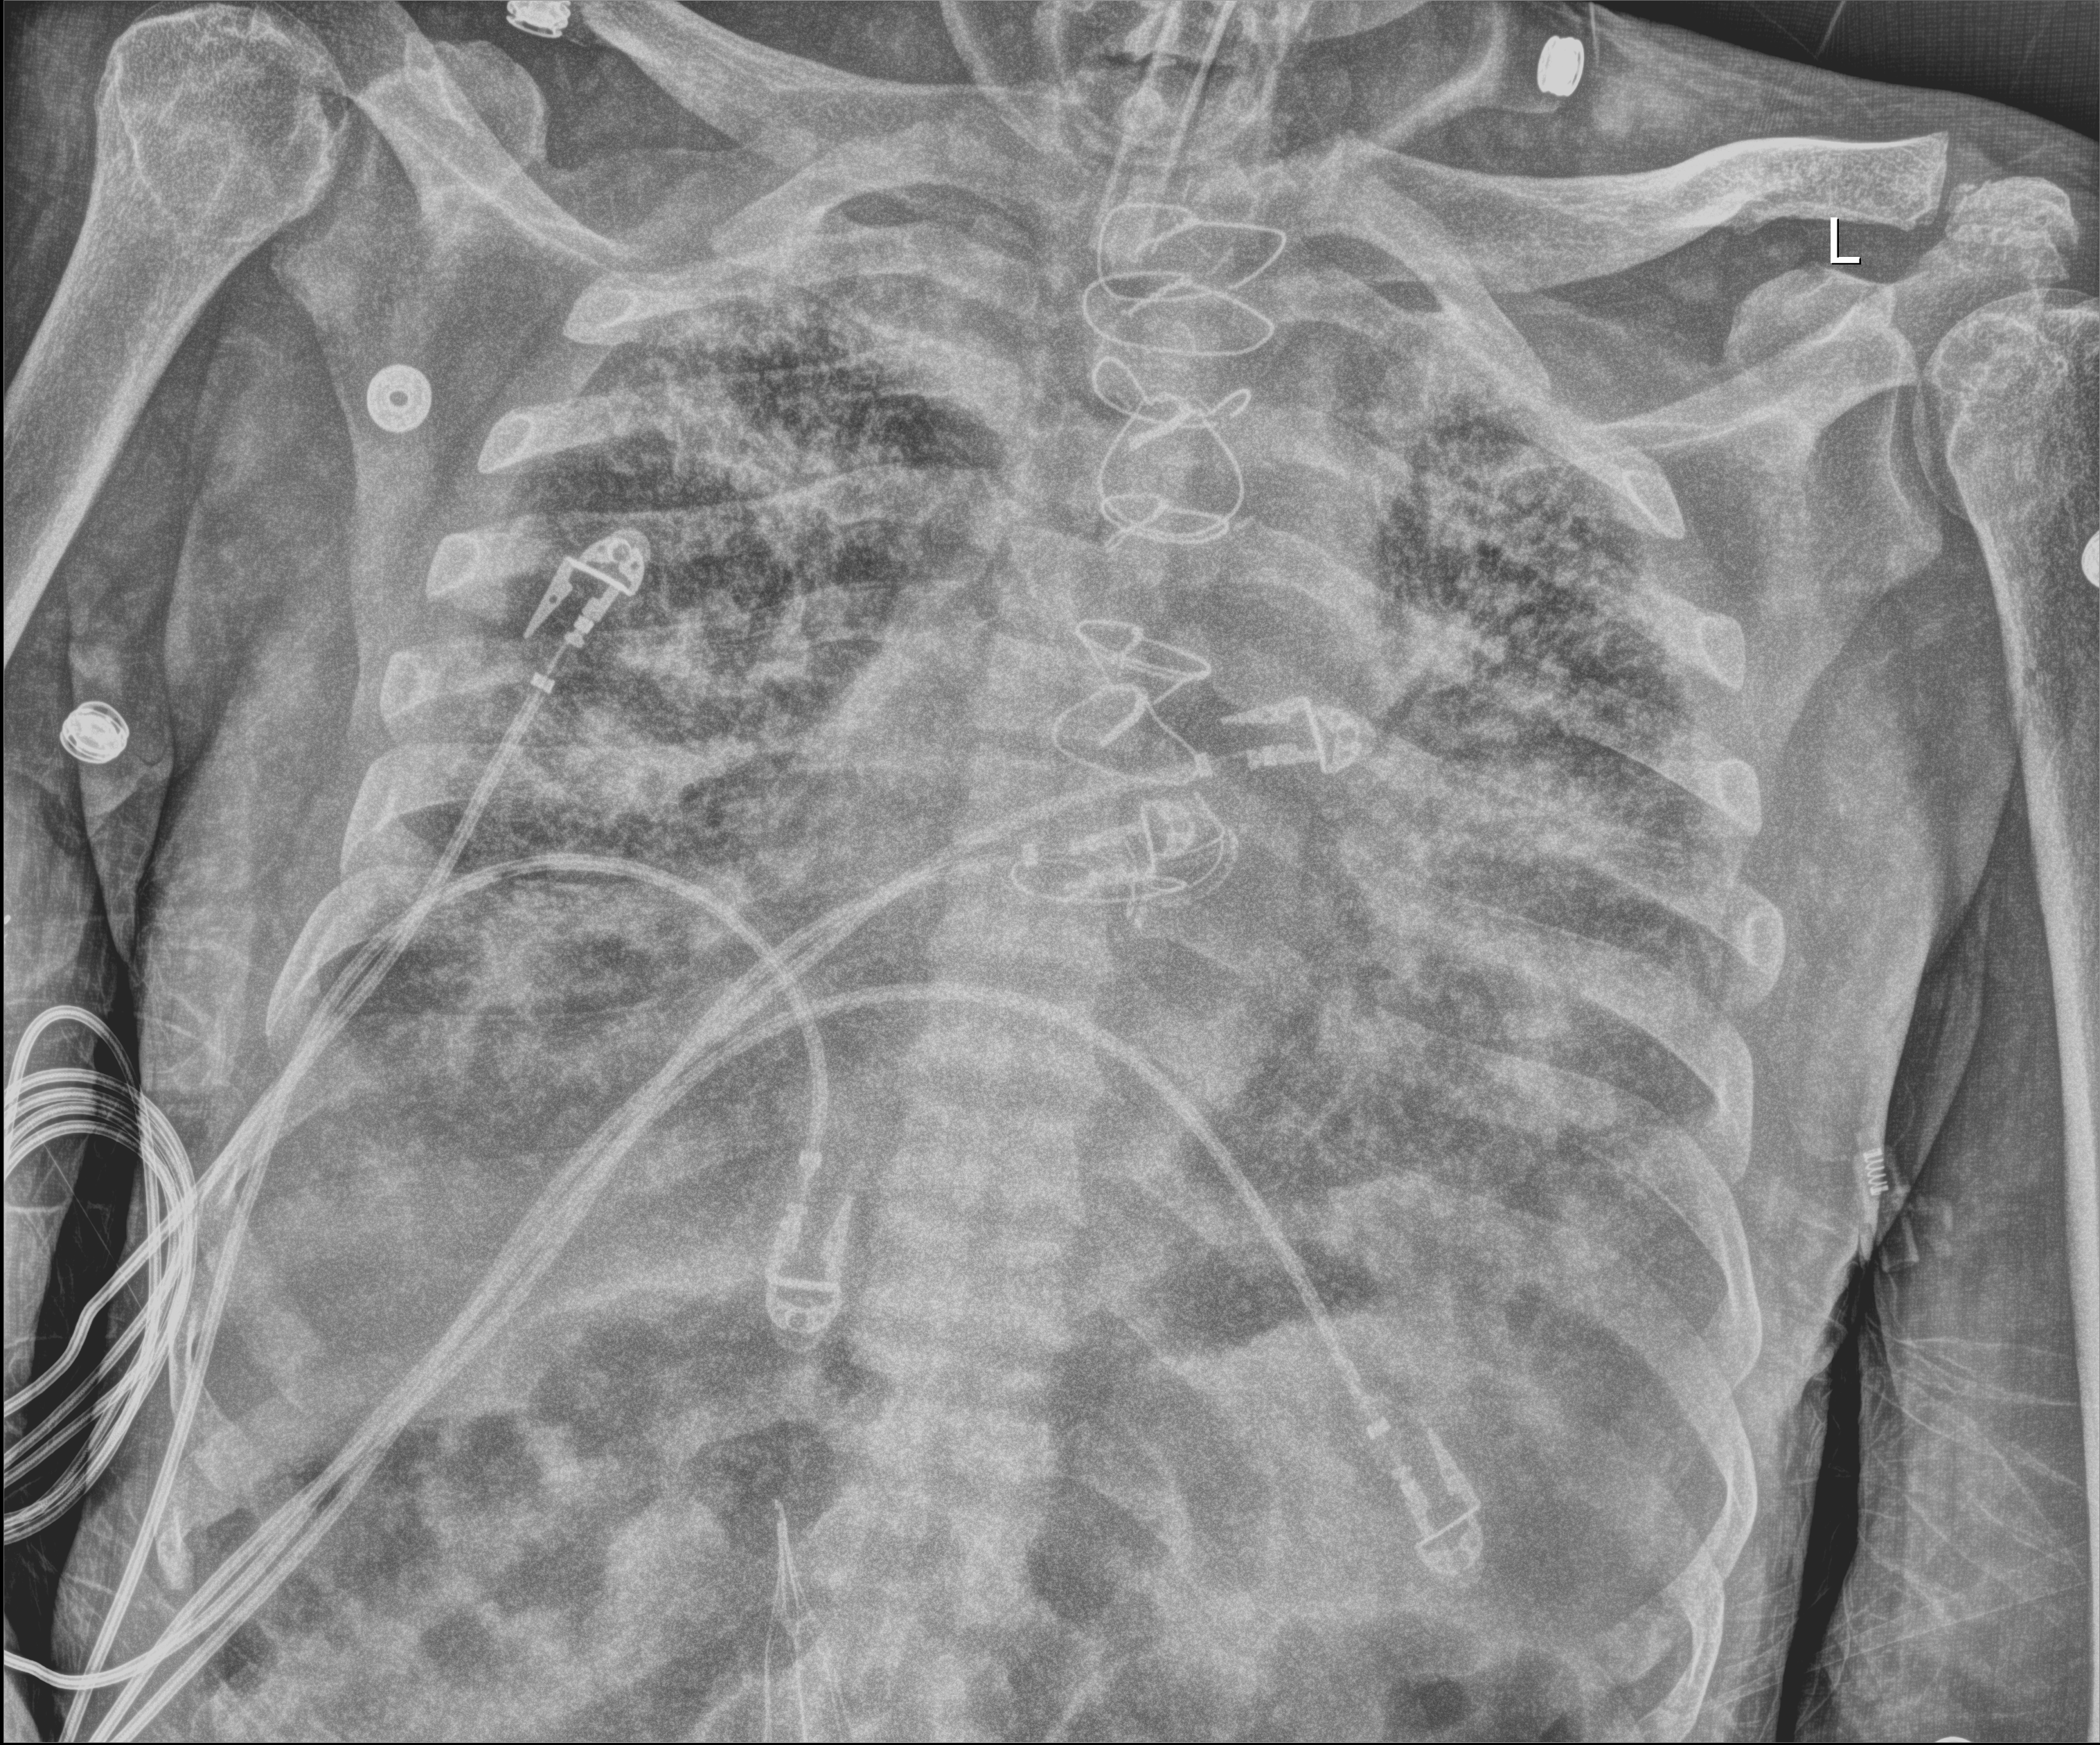
Chest X-ray (portable), anteroposterior (AP) projection. Patient hospitalised with COVID-19; male, aged 60–74 years.
Hospital-stay facts (about this admission, not read from this image; timing relative to this image not recorded): mechanically ventilated during this hospital stay: yes; other chronic lung disease (admission record): no; admitted to intensive care during this hospital stay: yes.